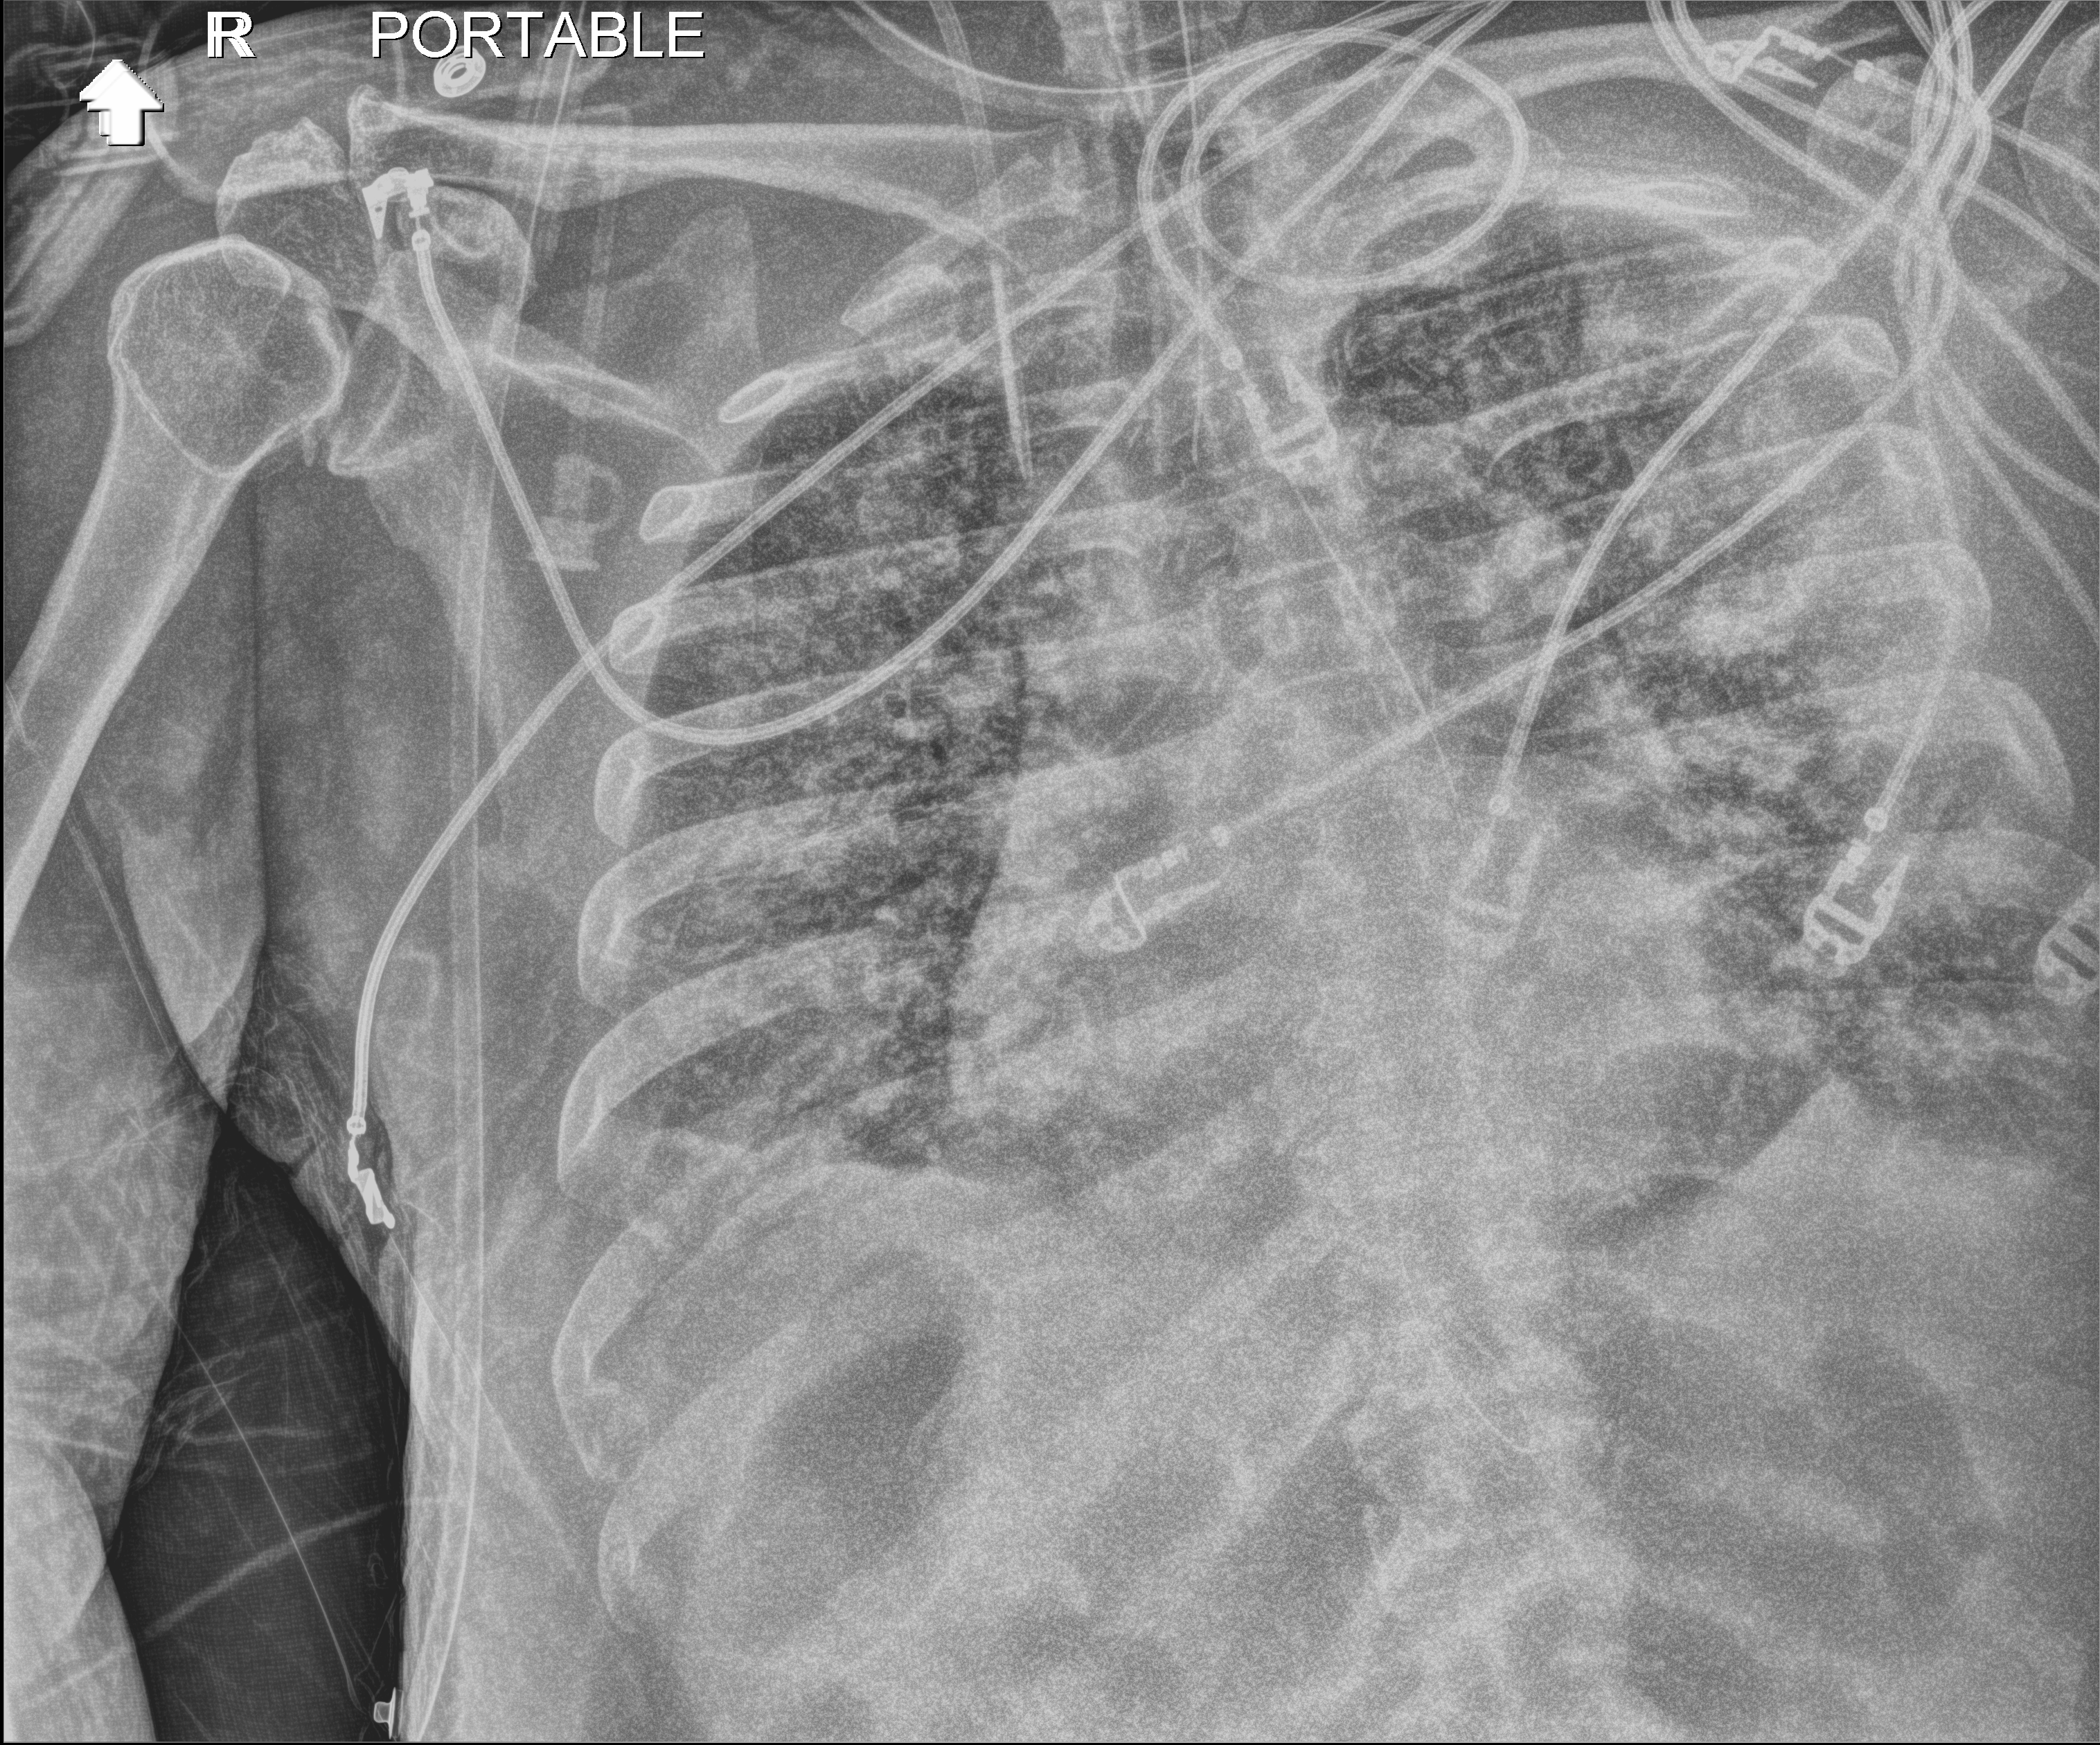
Bedside chest radiograph (digital radiography); anteroposterior (AP) projection. Patient hospitalised with COVID-19; male, aged 60–74 years.
Hospital-stay facts (about this admission, not read from this image; timing relative to this image not recorded): diabetes (admission record): no.